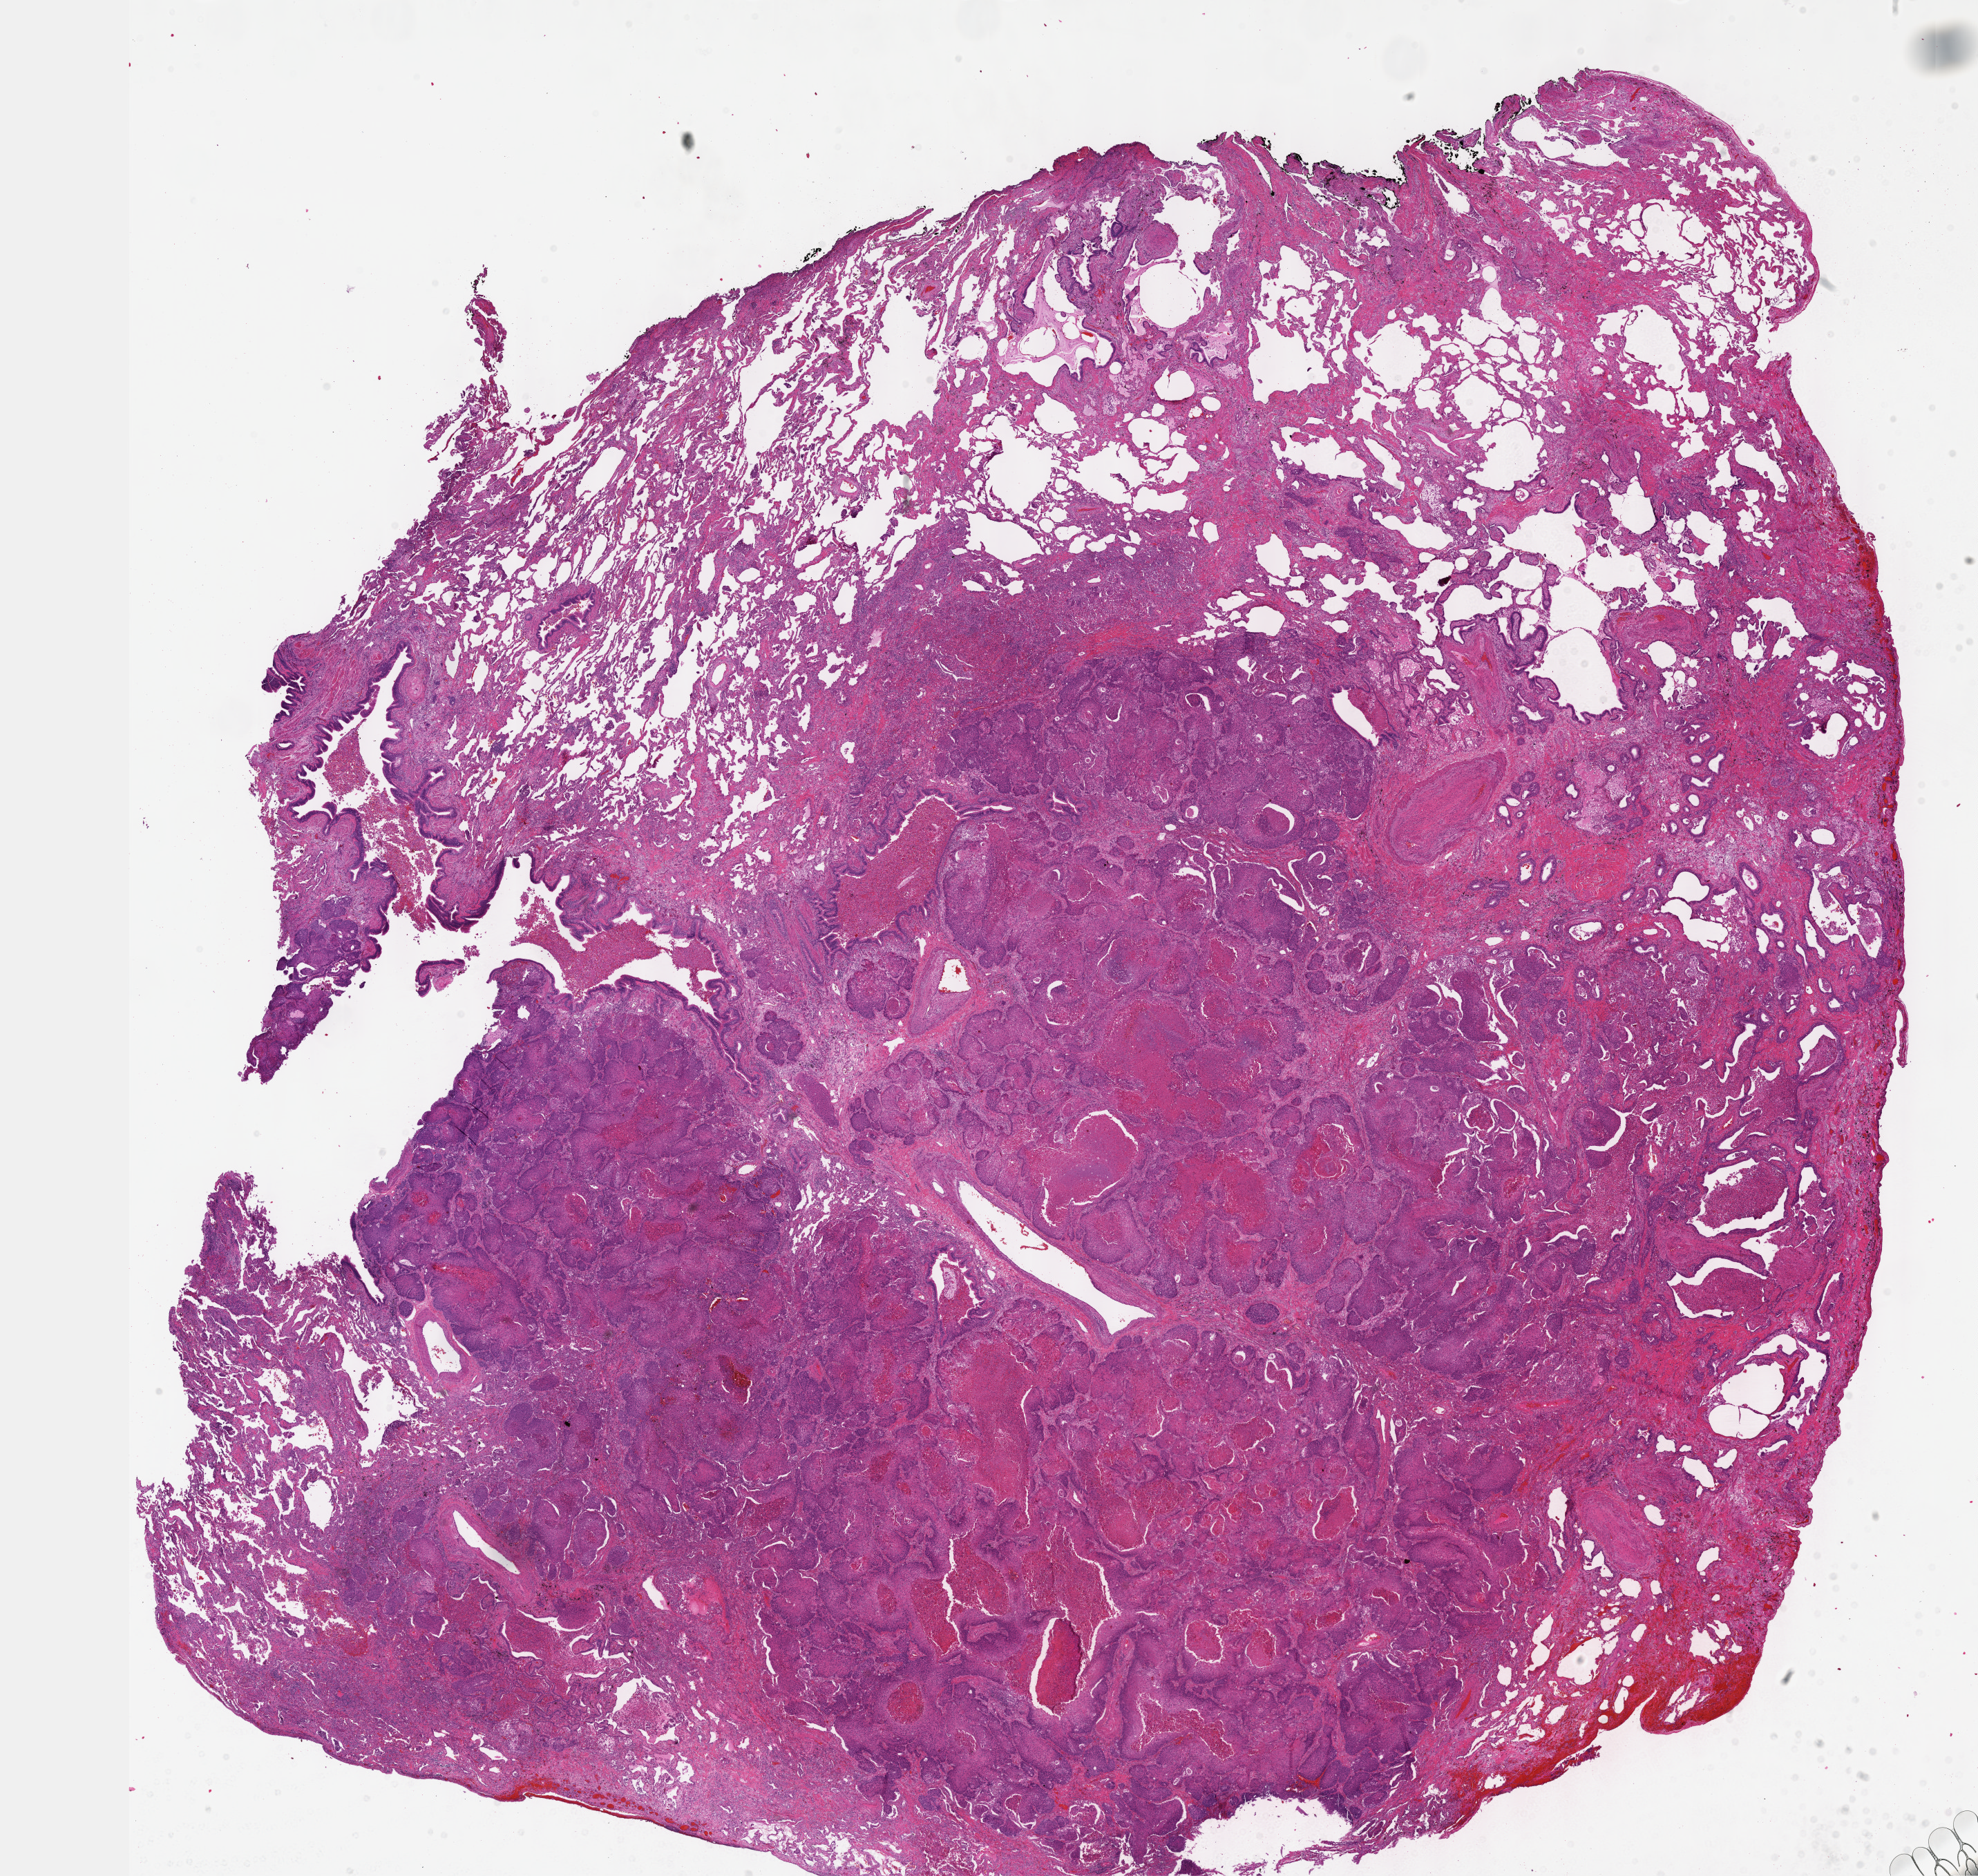
Hematoxylin and eosin (H&E) stained whole-slide image, low-resolution overview of the scanned area, about 23.1 x 21.9 mm (acquisition: 40x scan); FFPE section; primary tumour sample from the lung. Male patient; age at initial diagnosis 67 years.
• pathologic diagnosis: Squamous cell carcinoma, NOS (lower lobe, lung)
• AJCC pathologic stage: IIA
• TNM: T1a N1 MX